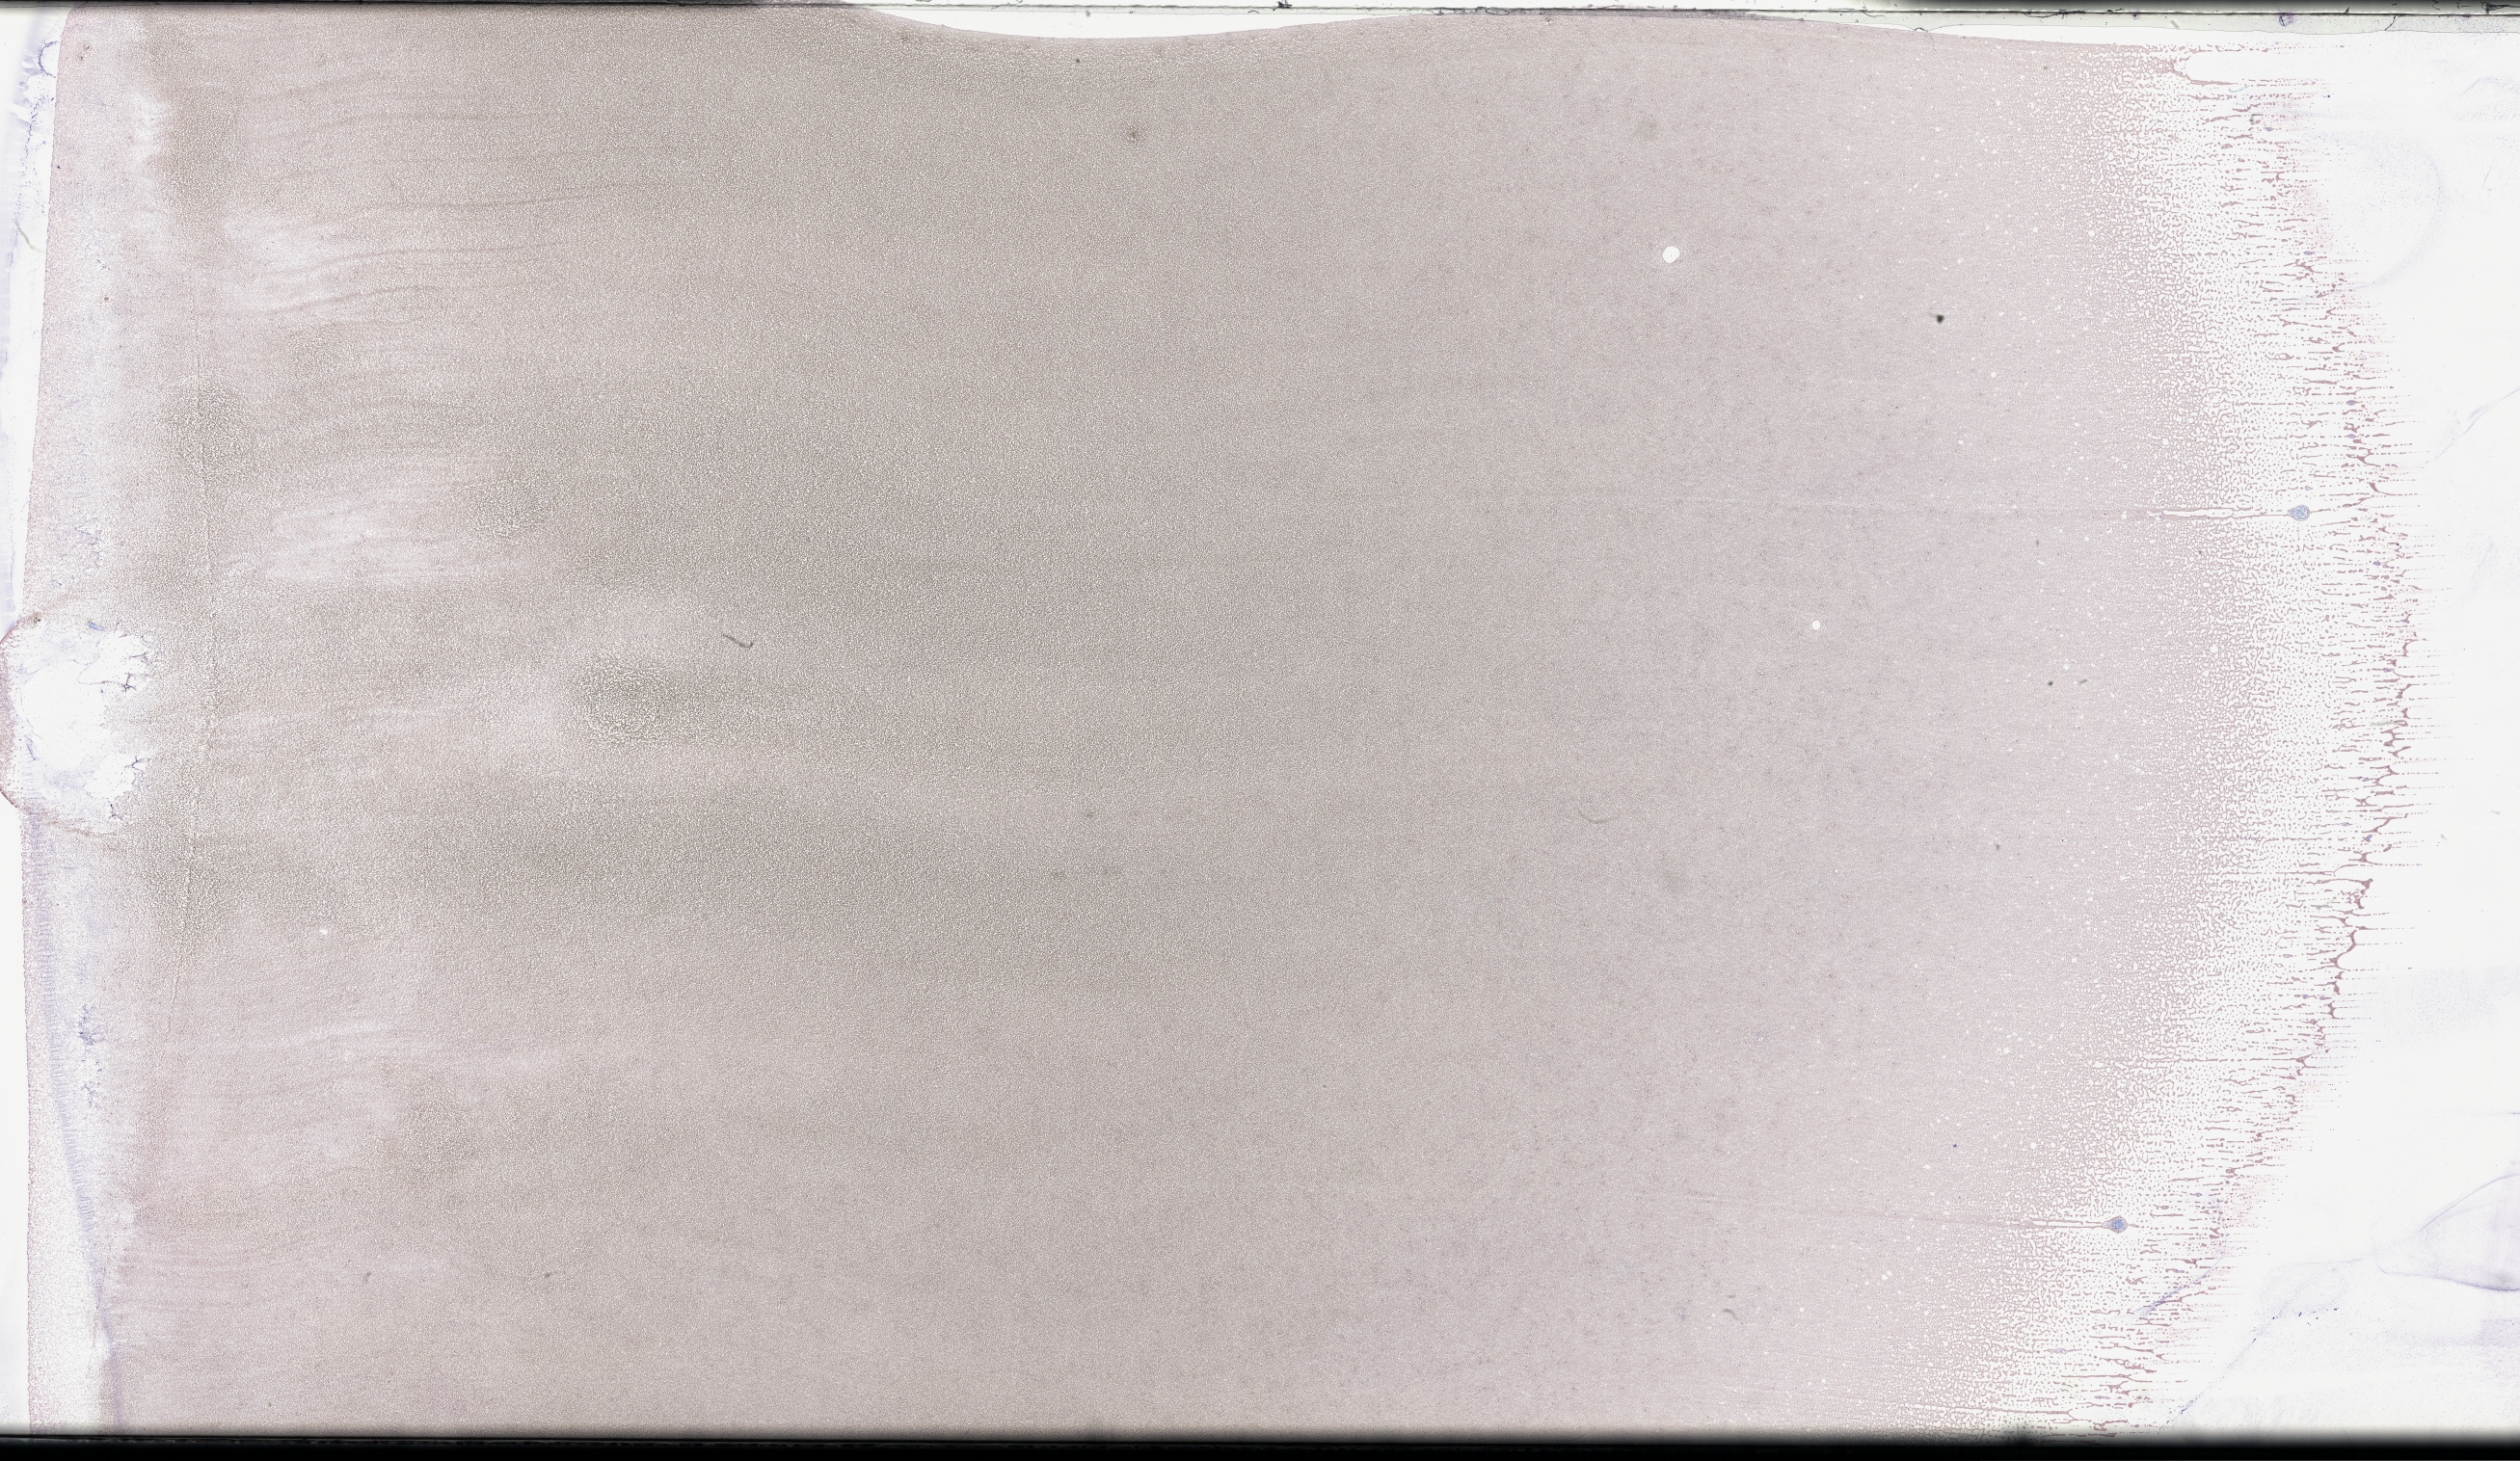
Wright-Giemsa-stained whole blood smear, whole-slide image — low-resolution overview of the scanned area, about 42.2 x 24.5 mm. EDTA-anticoagulated smear. Patient: male.
• patient diagnosis: Plasma Cell Myeloma